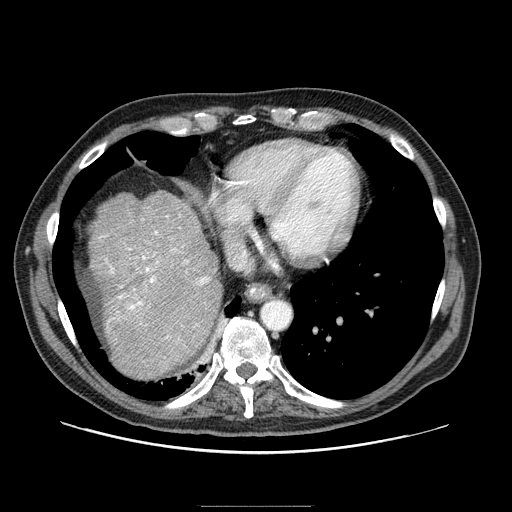
Contrast-enhanced abdominal CT (liver protocol), one axial slice. Position 78 of 99 along the scan axis. Reconstruction kernel STANDARD. One of 2 acquisitions stored at this slice position. Soft-tissue window (W 400 / L 40 HU). 512 × 512 image matrix, field of view 400 × 400 mm. Case-level facts recorded for this patient, not image findings: diagnosis: hepatocellular carcinoma (patient treated with transarterial chemoembolisation; whether this scan precedes or follows treatment is not stated here); TNM stage (as recorded): Stage-II; Child-Pugh class: A; tumour size: 3.2 cm.
Annotated regions visible in this slice (semi-automatically segmented with operator editing):
- liver parenchyma outside the tumour (the mass and vessels are separate outlines, so this box may not span the whole liver): bounding box [x1, y1, x2, y2] px = [89, 191, 222, 378]
- liver vessels: [100, 215, 210, 347]